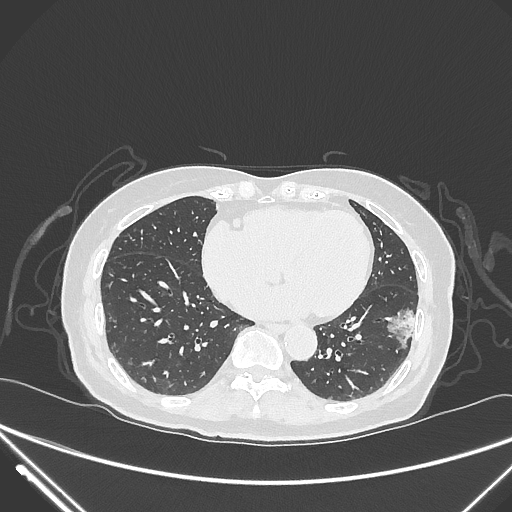
Chest CT, one axial slice. Slice 112 of 310 in the series (ordered by position). Lung window (W 1500 / L -600 HU). 512 × 512 image matrix. Patient: female, 82 years. Case-level facts recorded for this patient, not image findings: clinical TNM (as recorded): T1c N0 M0; histopathological grade: G2.
Outlined on this slice (bounding box drawn by a radiologist):
- lung tumour (recorded histology: adenocarcinoma): bounding box [x1, y1, x2, y2] px = [379, 301, 420, 354]